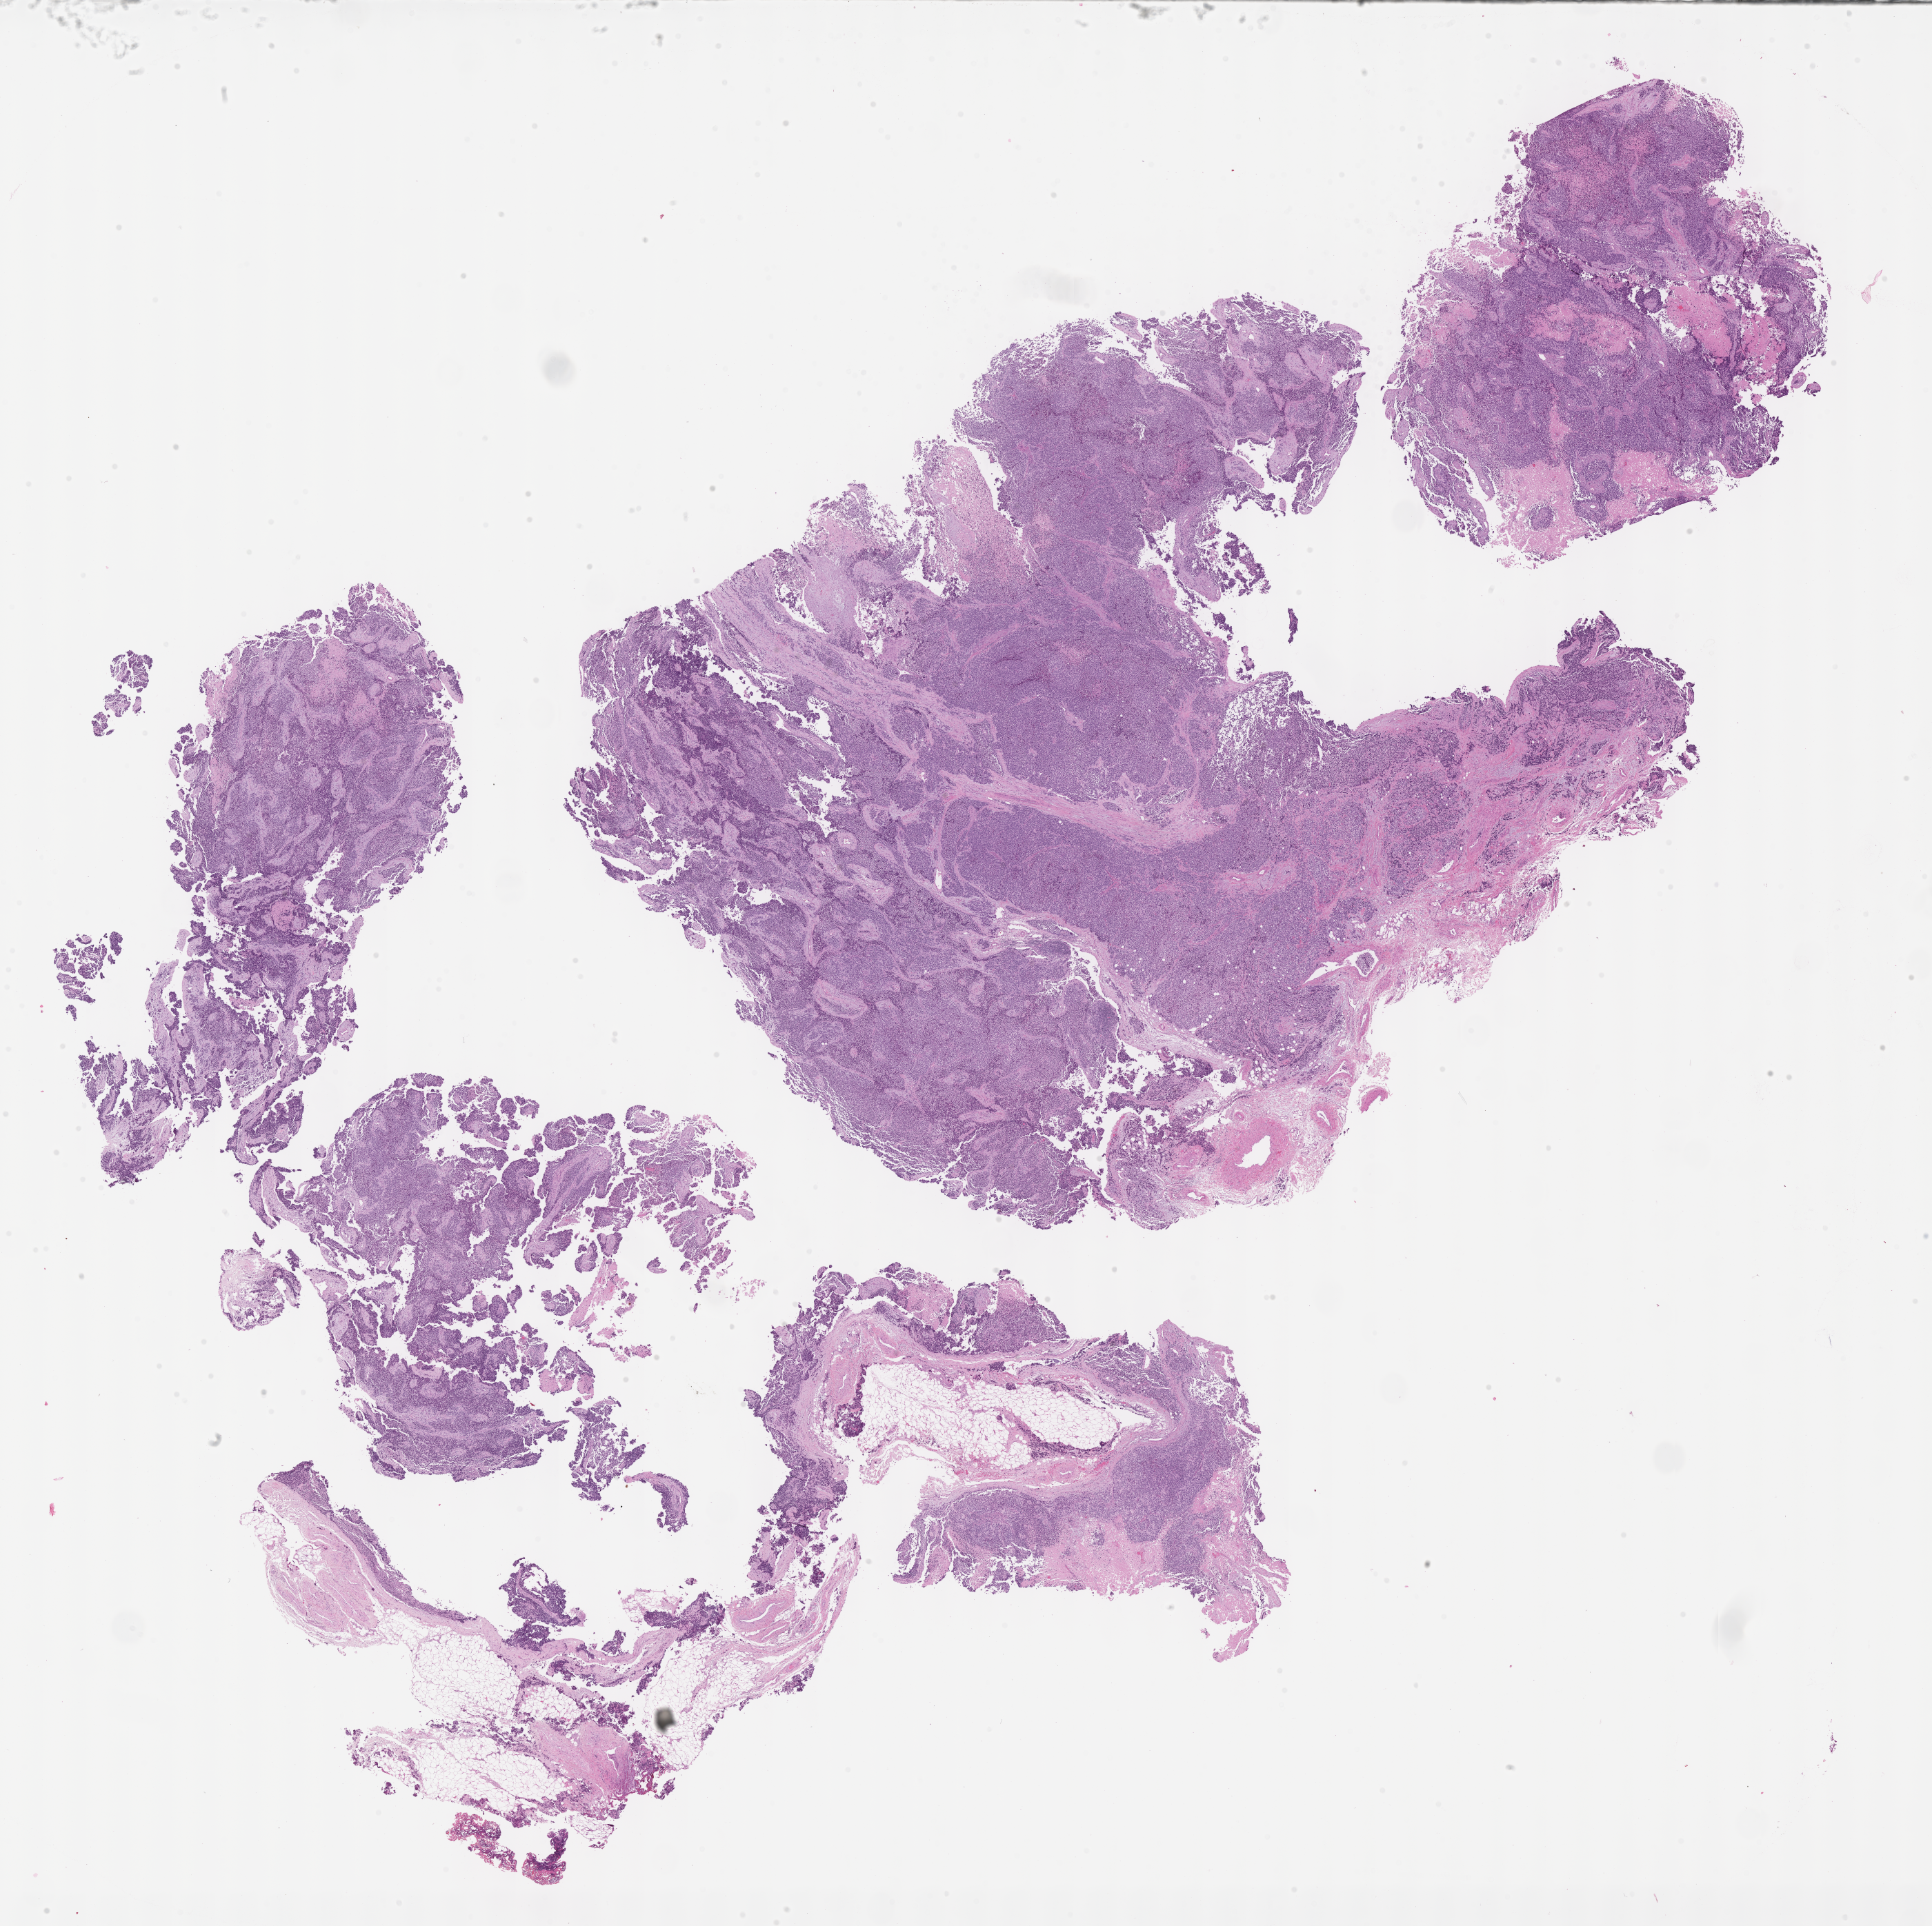
Digitized haematoxylin and eosin-stained section of tumor tissue, low-resolution overview of the scanned area, about 22.6 x 22.6 mm; formalin-fixed paraffin-embedded section; site: thigh, left upper. Female patient, age at diagnosis 13.9 years.
Diagnosis: rhabdomyosarcoma; histological classification: alveolar rhabdomyosarcoma.